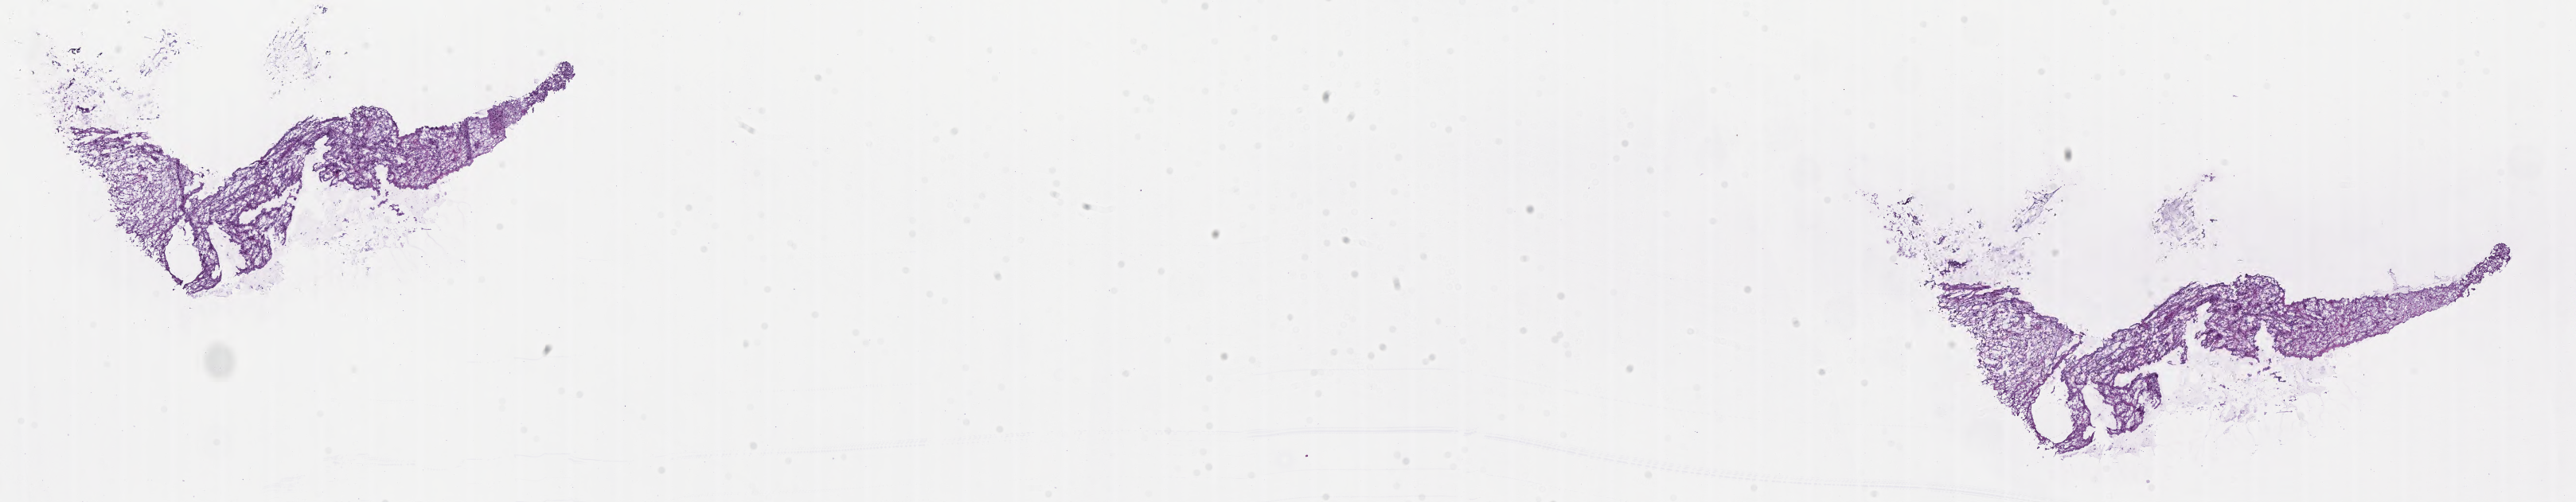
Haematoxylin and eosin whole-slide image of tumor tissue from the testis, shown as a low-resolution overview of the whole scanned area (about 26.2 x 5.1 mm). Frozen section. Patient male; age 109 months (9 years 1 month).
Diagnosis (ICD-O-3 morphology term): Embryonal rhabdomyosarcoma, NOS.